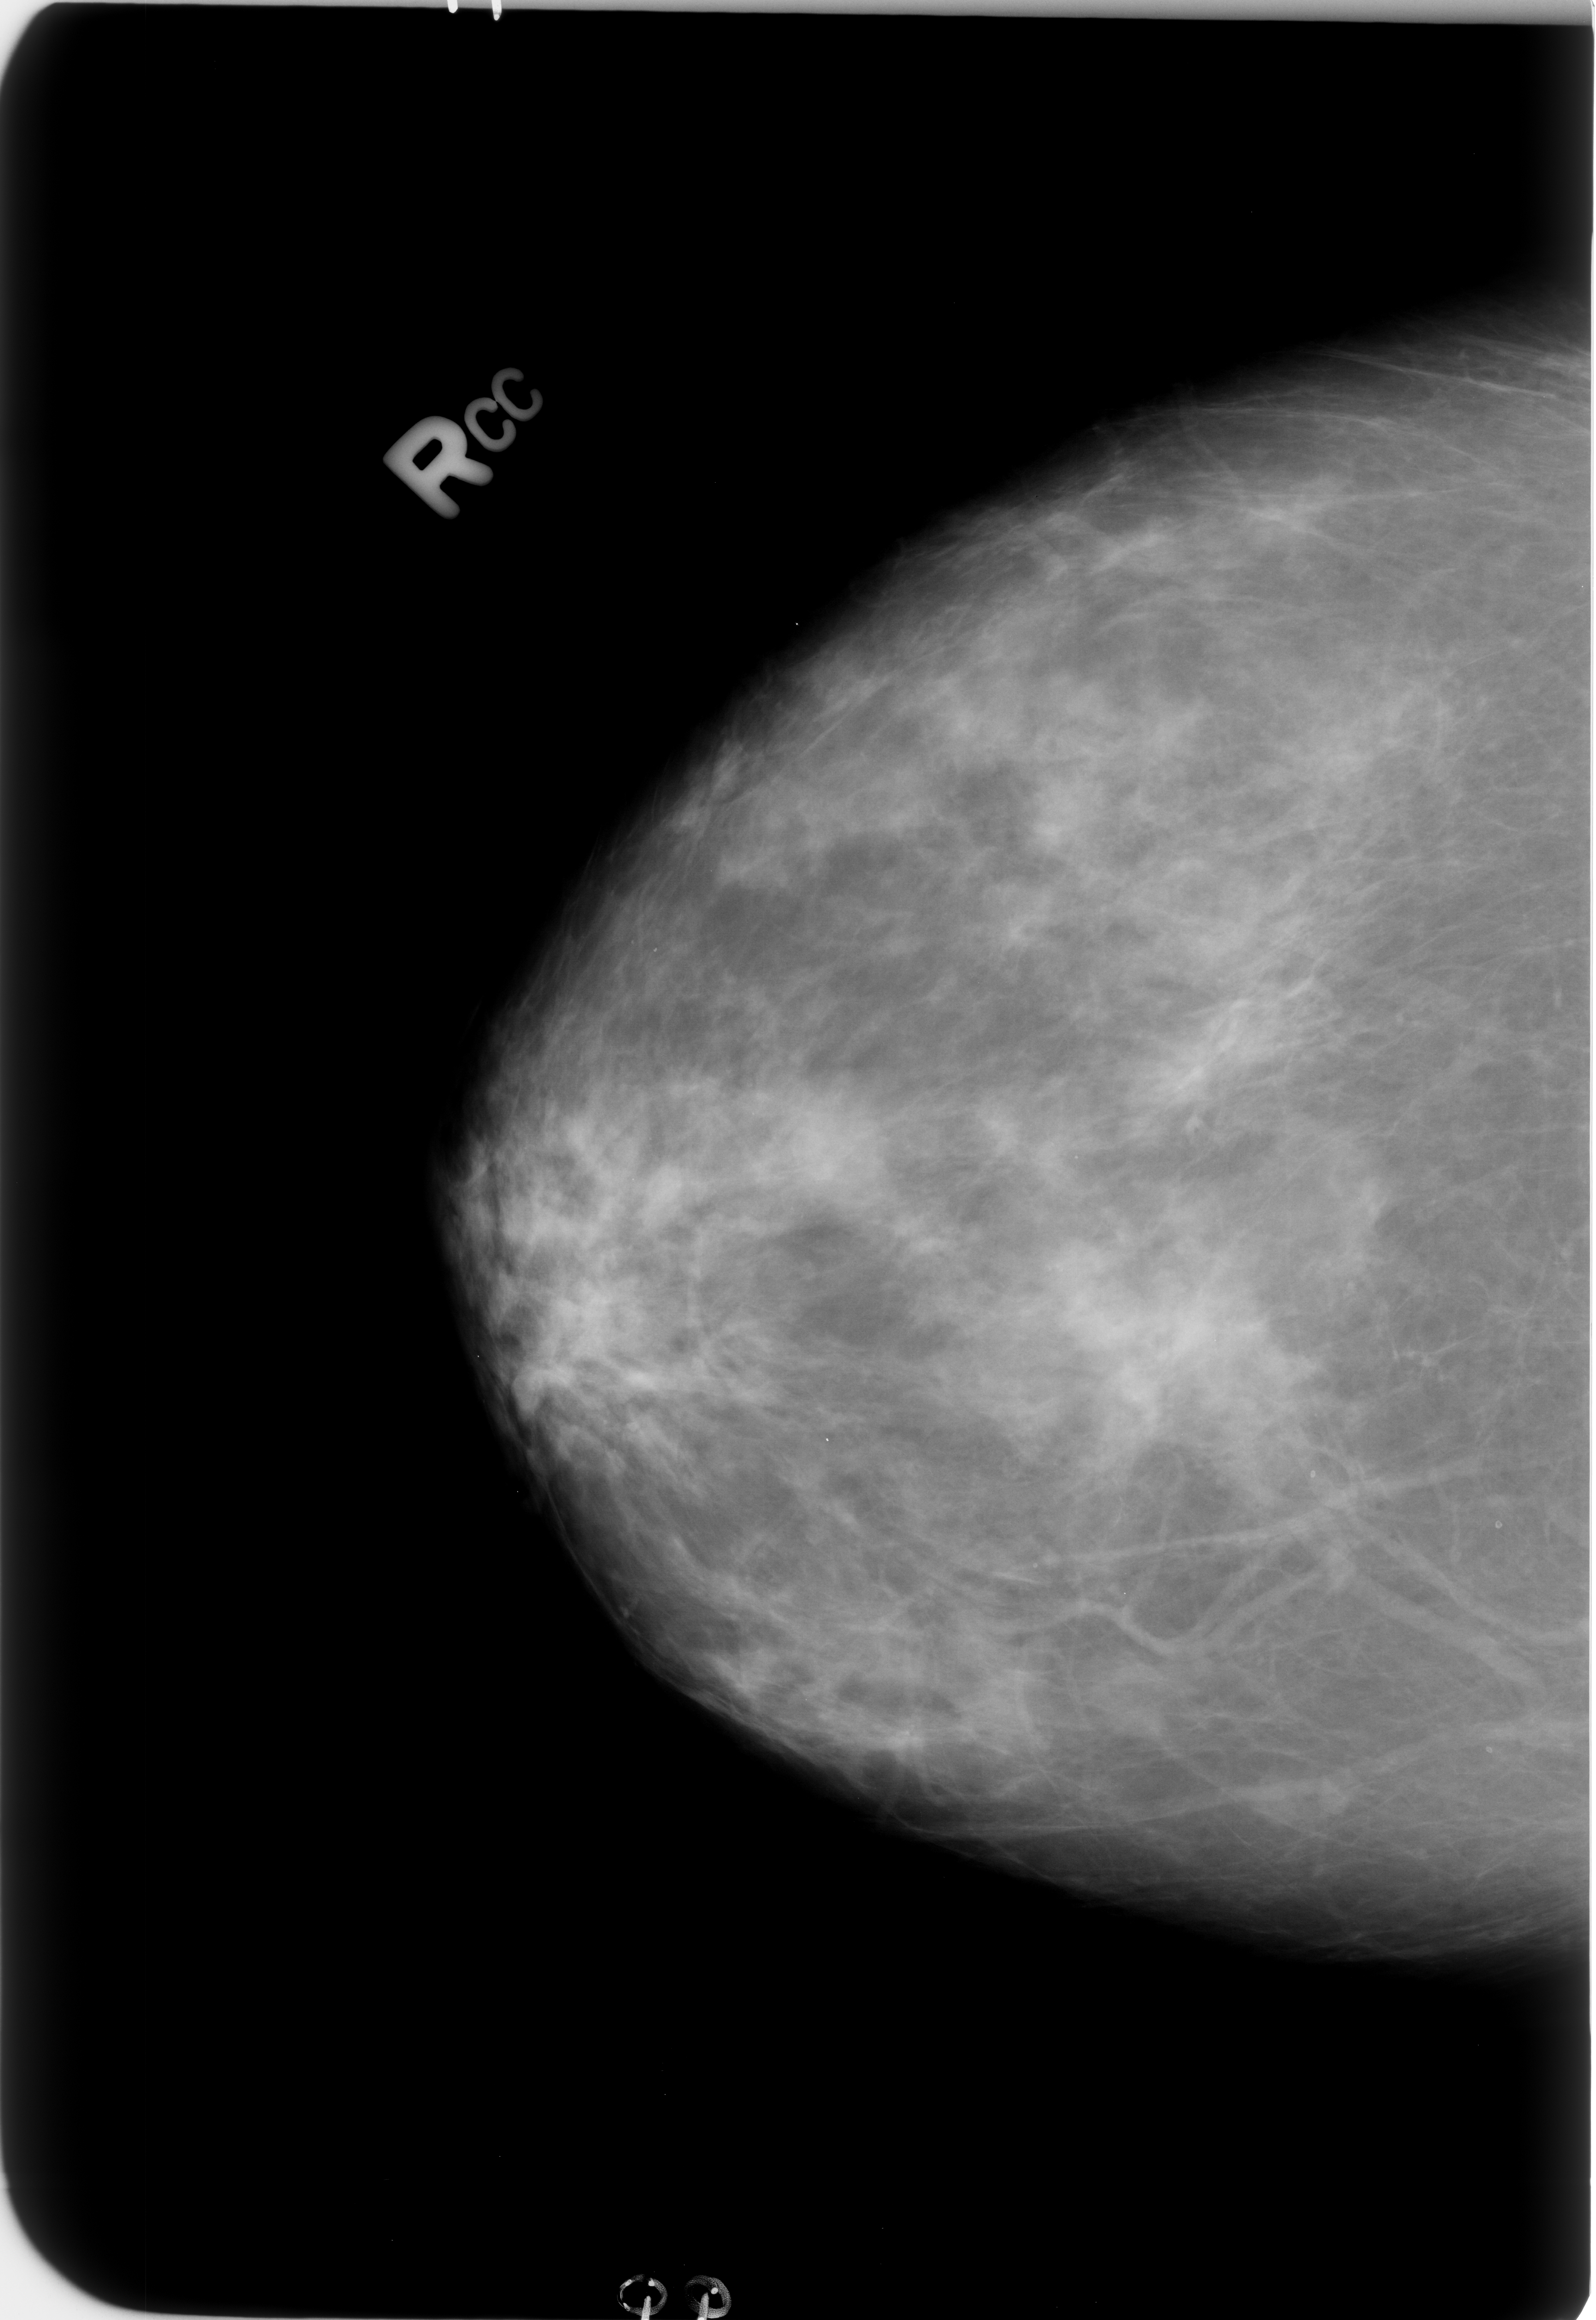
Scanned film-screen mammogram; right breast; CC view; BI-RADS breast density category 2 (scale 1–4); 1596 × 2320 image matrix.
Marked abnormalities (boxes around the expert regions of interest):
- Finding 1 of 3: calcifications, morphology lucent center; BI-RADS assessment category 2; subtlety rating 3 on a 1 (subtle) to 5 (obvious) scale; benign; no additional work-up was recommended (outcome (as recorded, no biopsy): benign without callback): bounding box <1309,1464,1323,1484> (left, top, right, bottom; pixels)
- Finding 2 of 3: calcifications, morphology lucent center; BI-RADS assessment category 2; benign; no additional work-up was recommended (outcome (as recorded, no biopsy): benign without callback): <1473,1740,1497,1761>
- Finding 3 of 3: calcifications, morphology lucent center; BI-RADS assessment category 2; subtlety rating 3 on a 1 (subtle) to 5 (obvious) scale; benign; no additional work-up was recommended (outcome (as recorded, no biopsy): benign without callback): <1489,1512,1510,1533>